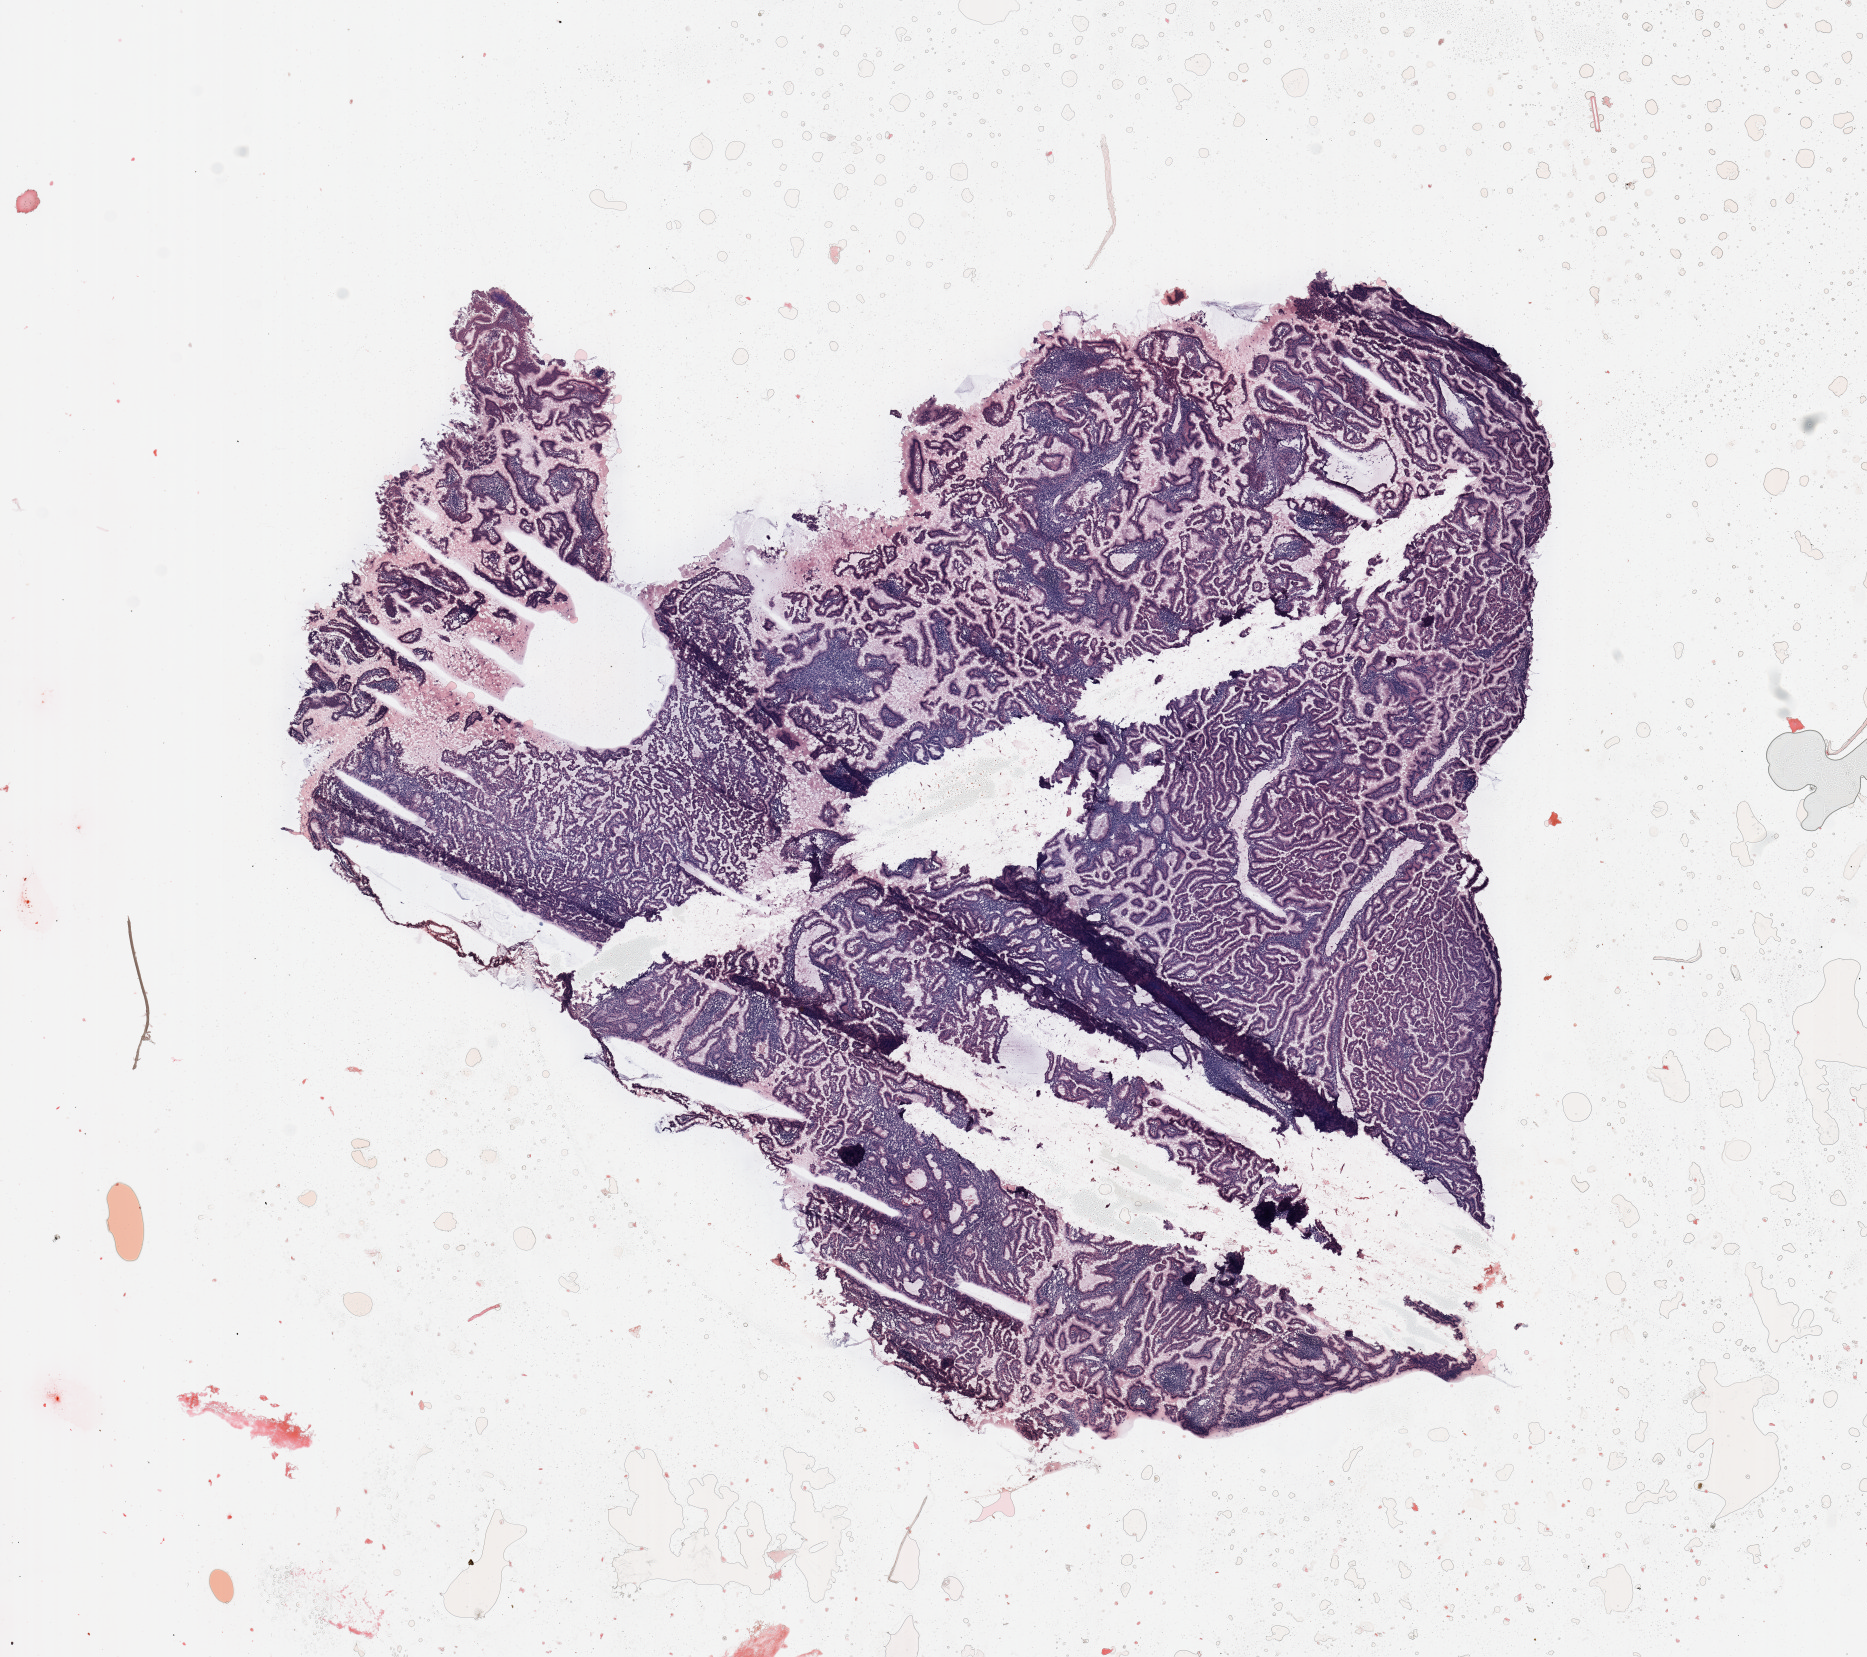
H&E whole-slide image — low-resolution overview of the scanned area, about 14.8 x 13.1 mm (acquisition: 20x scan); tumour tissue sample, sampled site: uterus. 61-year-old female patient. Histologic grade: G1 (well differentiated). Composition of this section per pathologist review: tumour nuclei 90%, necrosis 0%.
AJCC pathologic stage: I. Histologic diagnosis: Endometrioid adenocarcinoma, NOS.